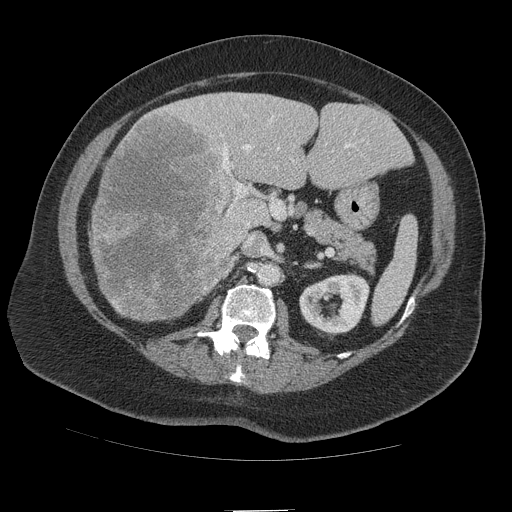
Contrast-enhanced abdominal CT (liver protocol), one axial slice. Position 53 of 109 along the scan axis. 140 kVp. Soft-tissue window (W 400 / L 40 HU). 2.5 mm slice thickness. 512 × 512 image matrix. Case-level facts recorded for this patient, not image findings: diagnosis: hepatocellular carcinoma (patient treated with transarterial chemoembolisation; whether this scan precedes or follows treatment is not stated here); TNM stage (as recorded): Stage-IVB; Child-Pugh class: A; tumour differentiation: poorly differentiated.
Outlined on this slice (semi-automatic segmentation, software-assisted and operator-edited):
- liver parenchyma outside the tumour (the mass and vessels are separate outlines, so this box may not span the whole liver): bounding box (x1, y1, x2, y2) in pixels: (90, 92, 412, 322)
- mass: (90, 109, 248, 322)
- liver vessels: (220, 116, 351, 226)